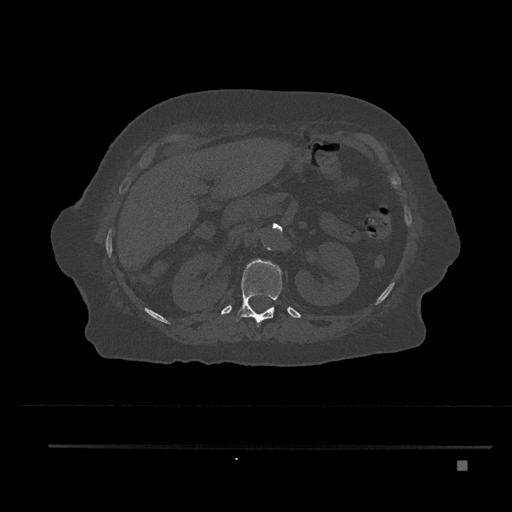
CT including the spine, one axial slice. Position 260 of 797 along the scan axis. Reconstruction kernel Br40s/3. Bone window (W 1800 / L 400 HU). 512 × 512 image matrix. Female patient, age 76 years. Case-level facts recorded for this patient, not image findings: primary cancer: lung; vertebrae with lytic lesions (as recorded): T11, L3.
Structures marked on this image (semi-automatic segmentation, software-assisted and operator-edited):
- T12 vertebra: bounding box [x1, y1, x2, y2] px = [235, 259, 282, 326]